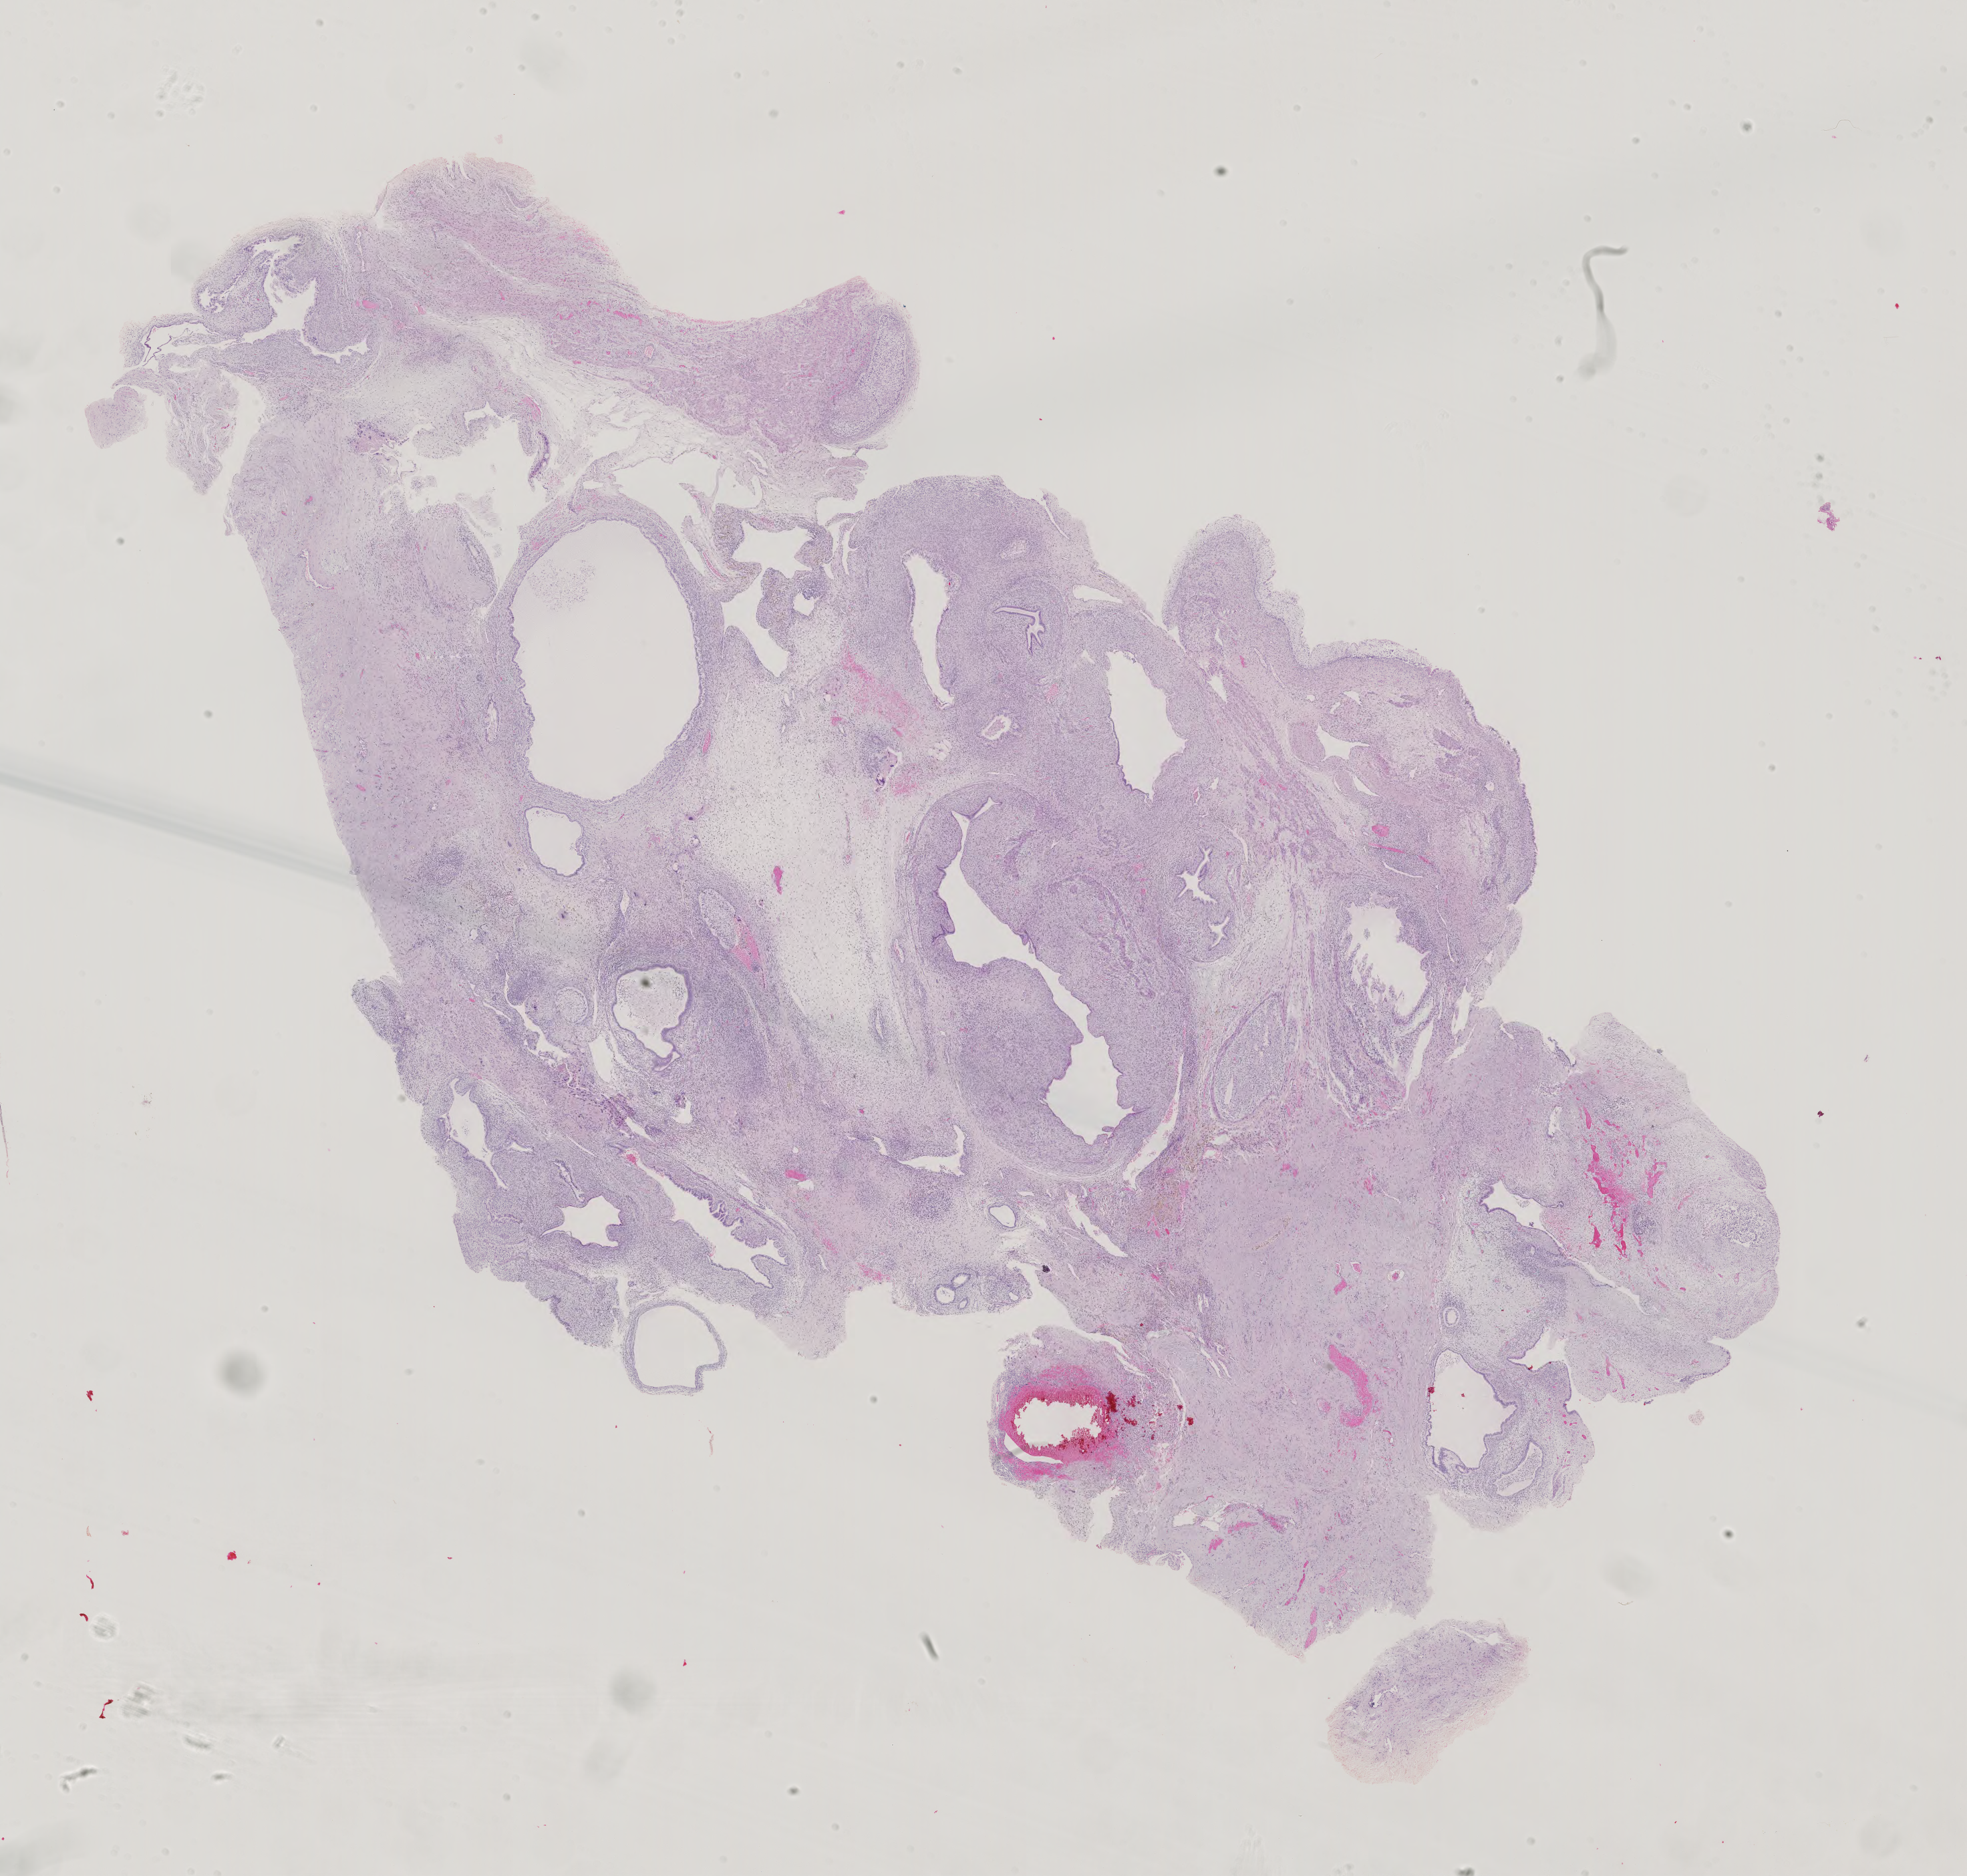
H&E whole-slide image, whole scanned area (about 21.5 x 20.5 mm) shown as a low-resolution overview. Male patient.
* specimen: formalin-fixed paraffin-embedded (FFPE) diagnostic section; sample: primary tumour, testis